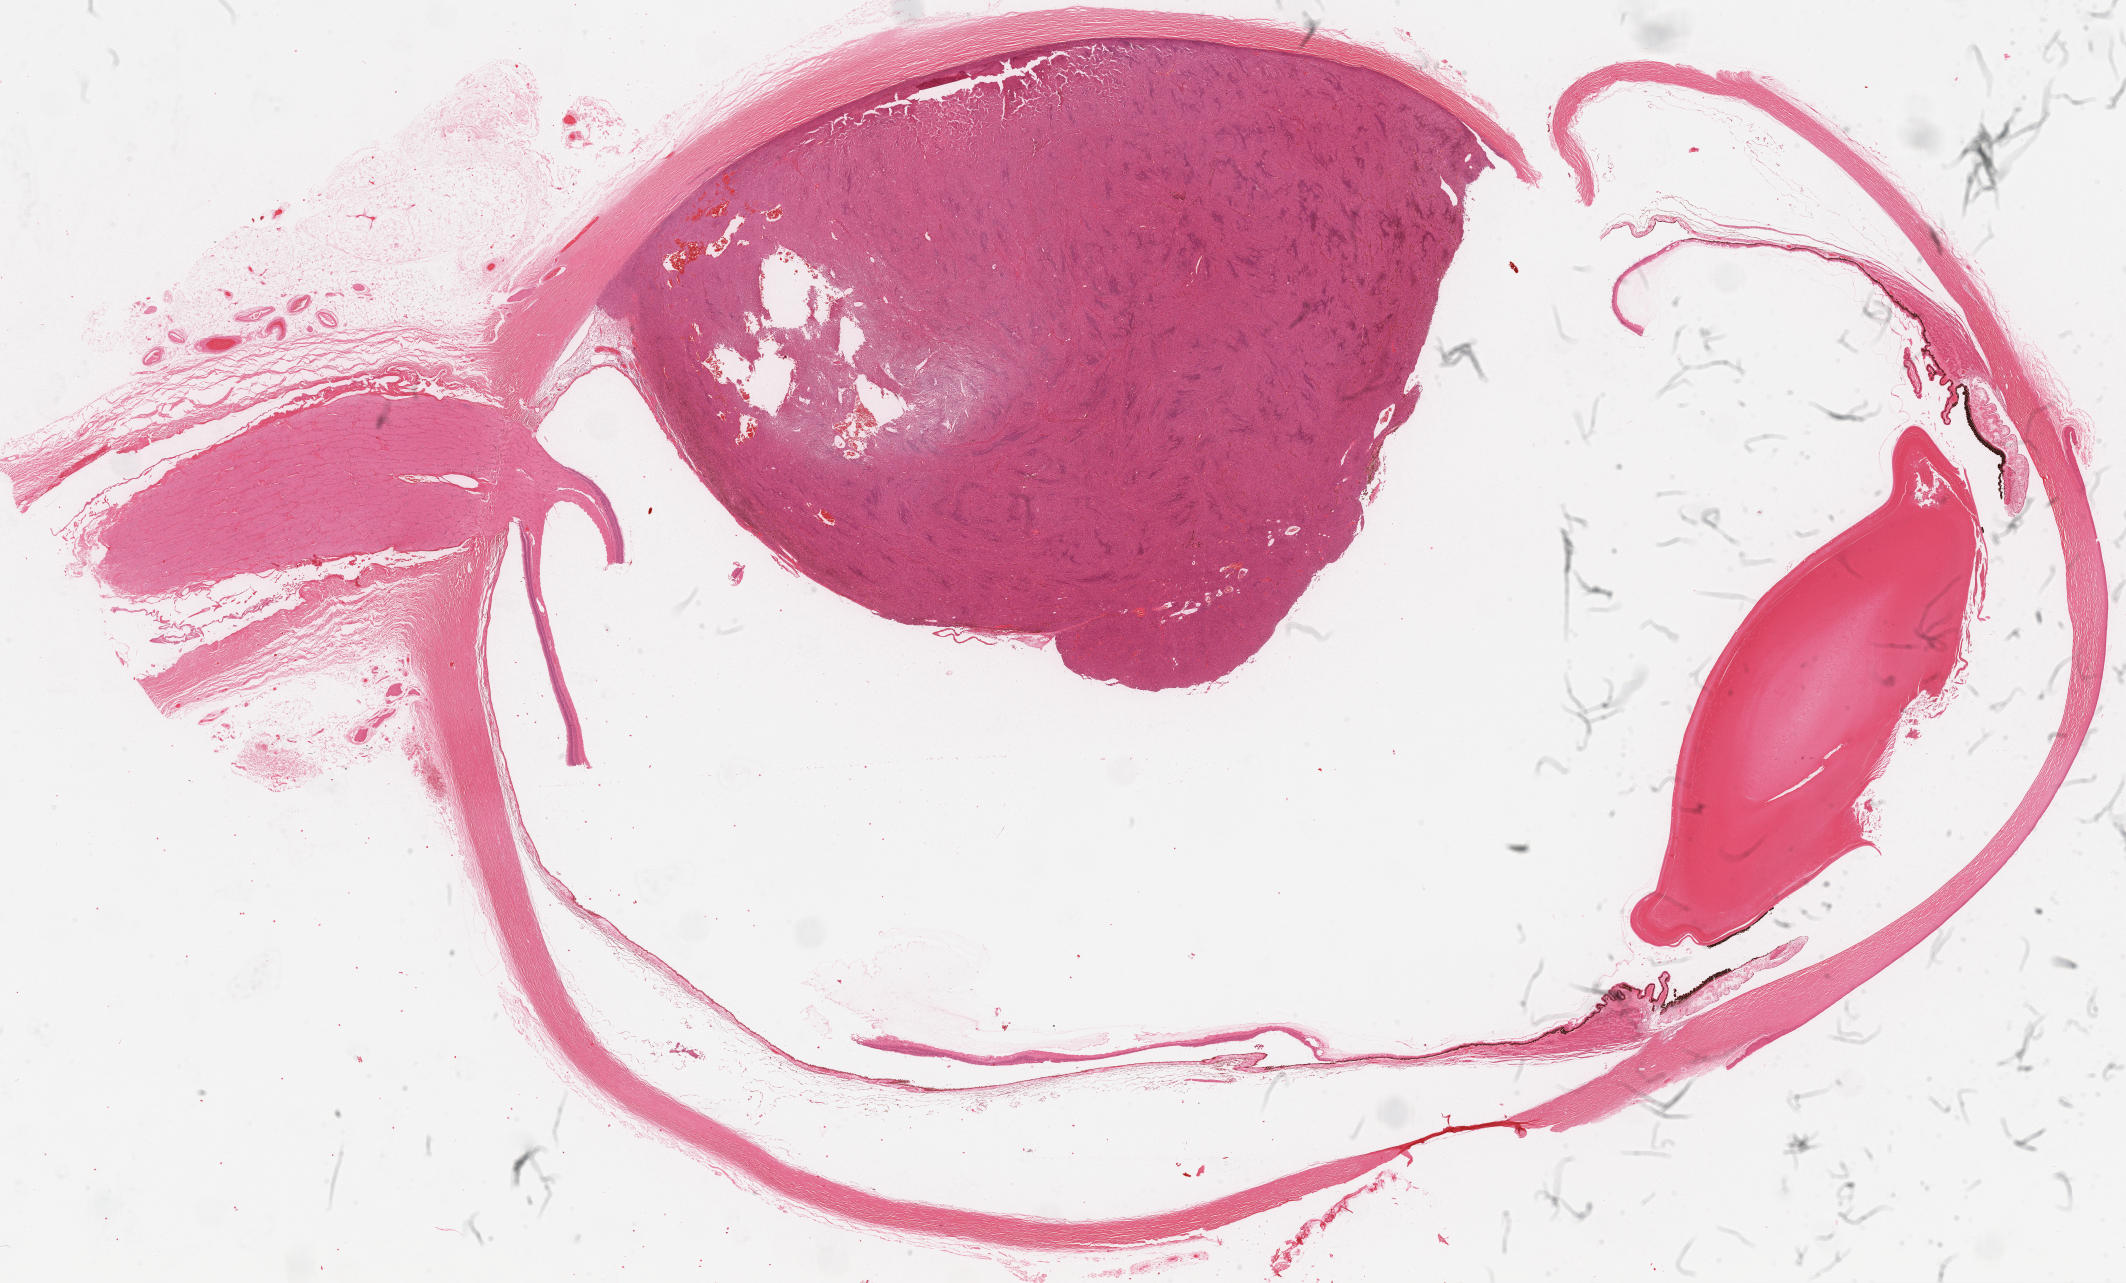
Whole-slide histology image, H&E, shown as a low-resolution overview of the whole scanned area (about 34.3 x 20.7 mm). Formalin-fixed paraffin-embedded (FFPE) diagnostic section. Primary tumour sample from the uvea. Patient: female, age at initial diagnosis 56 years. Slide review estimates, as recorded: tumour cells 50%, tumour nuclei 60%, normal cells 50%, stromal cells 0%, necrosis 0%. Inflammatory infiltration, as recorded: lymphocyte infiltration 1%, monocyte infiltration 0%, neutrophil infiltration 0%.
AJCC pathologic stage: IIB. Pathologic diagnosis: Mixed epithelioid and spindle cell melanoma (choroid).